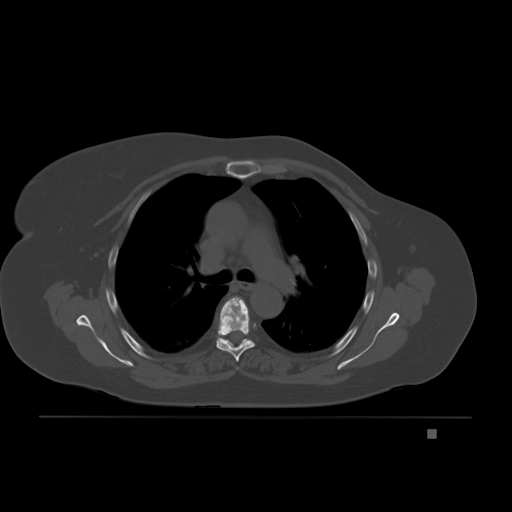
CT including the spine, one axial slice. Position 144 of 221 along the scan axis. Bone window (W 1800 / L 400 HU). 3 mm slice thickness. 512 × 512 image matrix, field of view 474 × 474 mm. Female patient, age 63 years. From the clinical record (not read from this slice): primary cancer: breast.
Annotated regions visible in this slice (semi-automatically segmented with operator editing):
- T5 vertebra: box from (x=216, y=297) to (x=255, y=362) px
- T6 vertebra: (x=220, y=338)–(x=247, y=343)